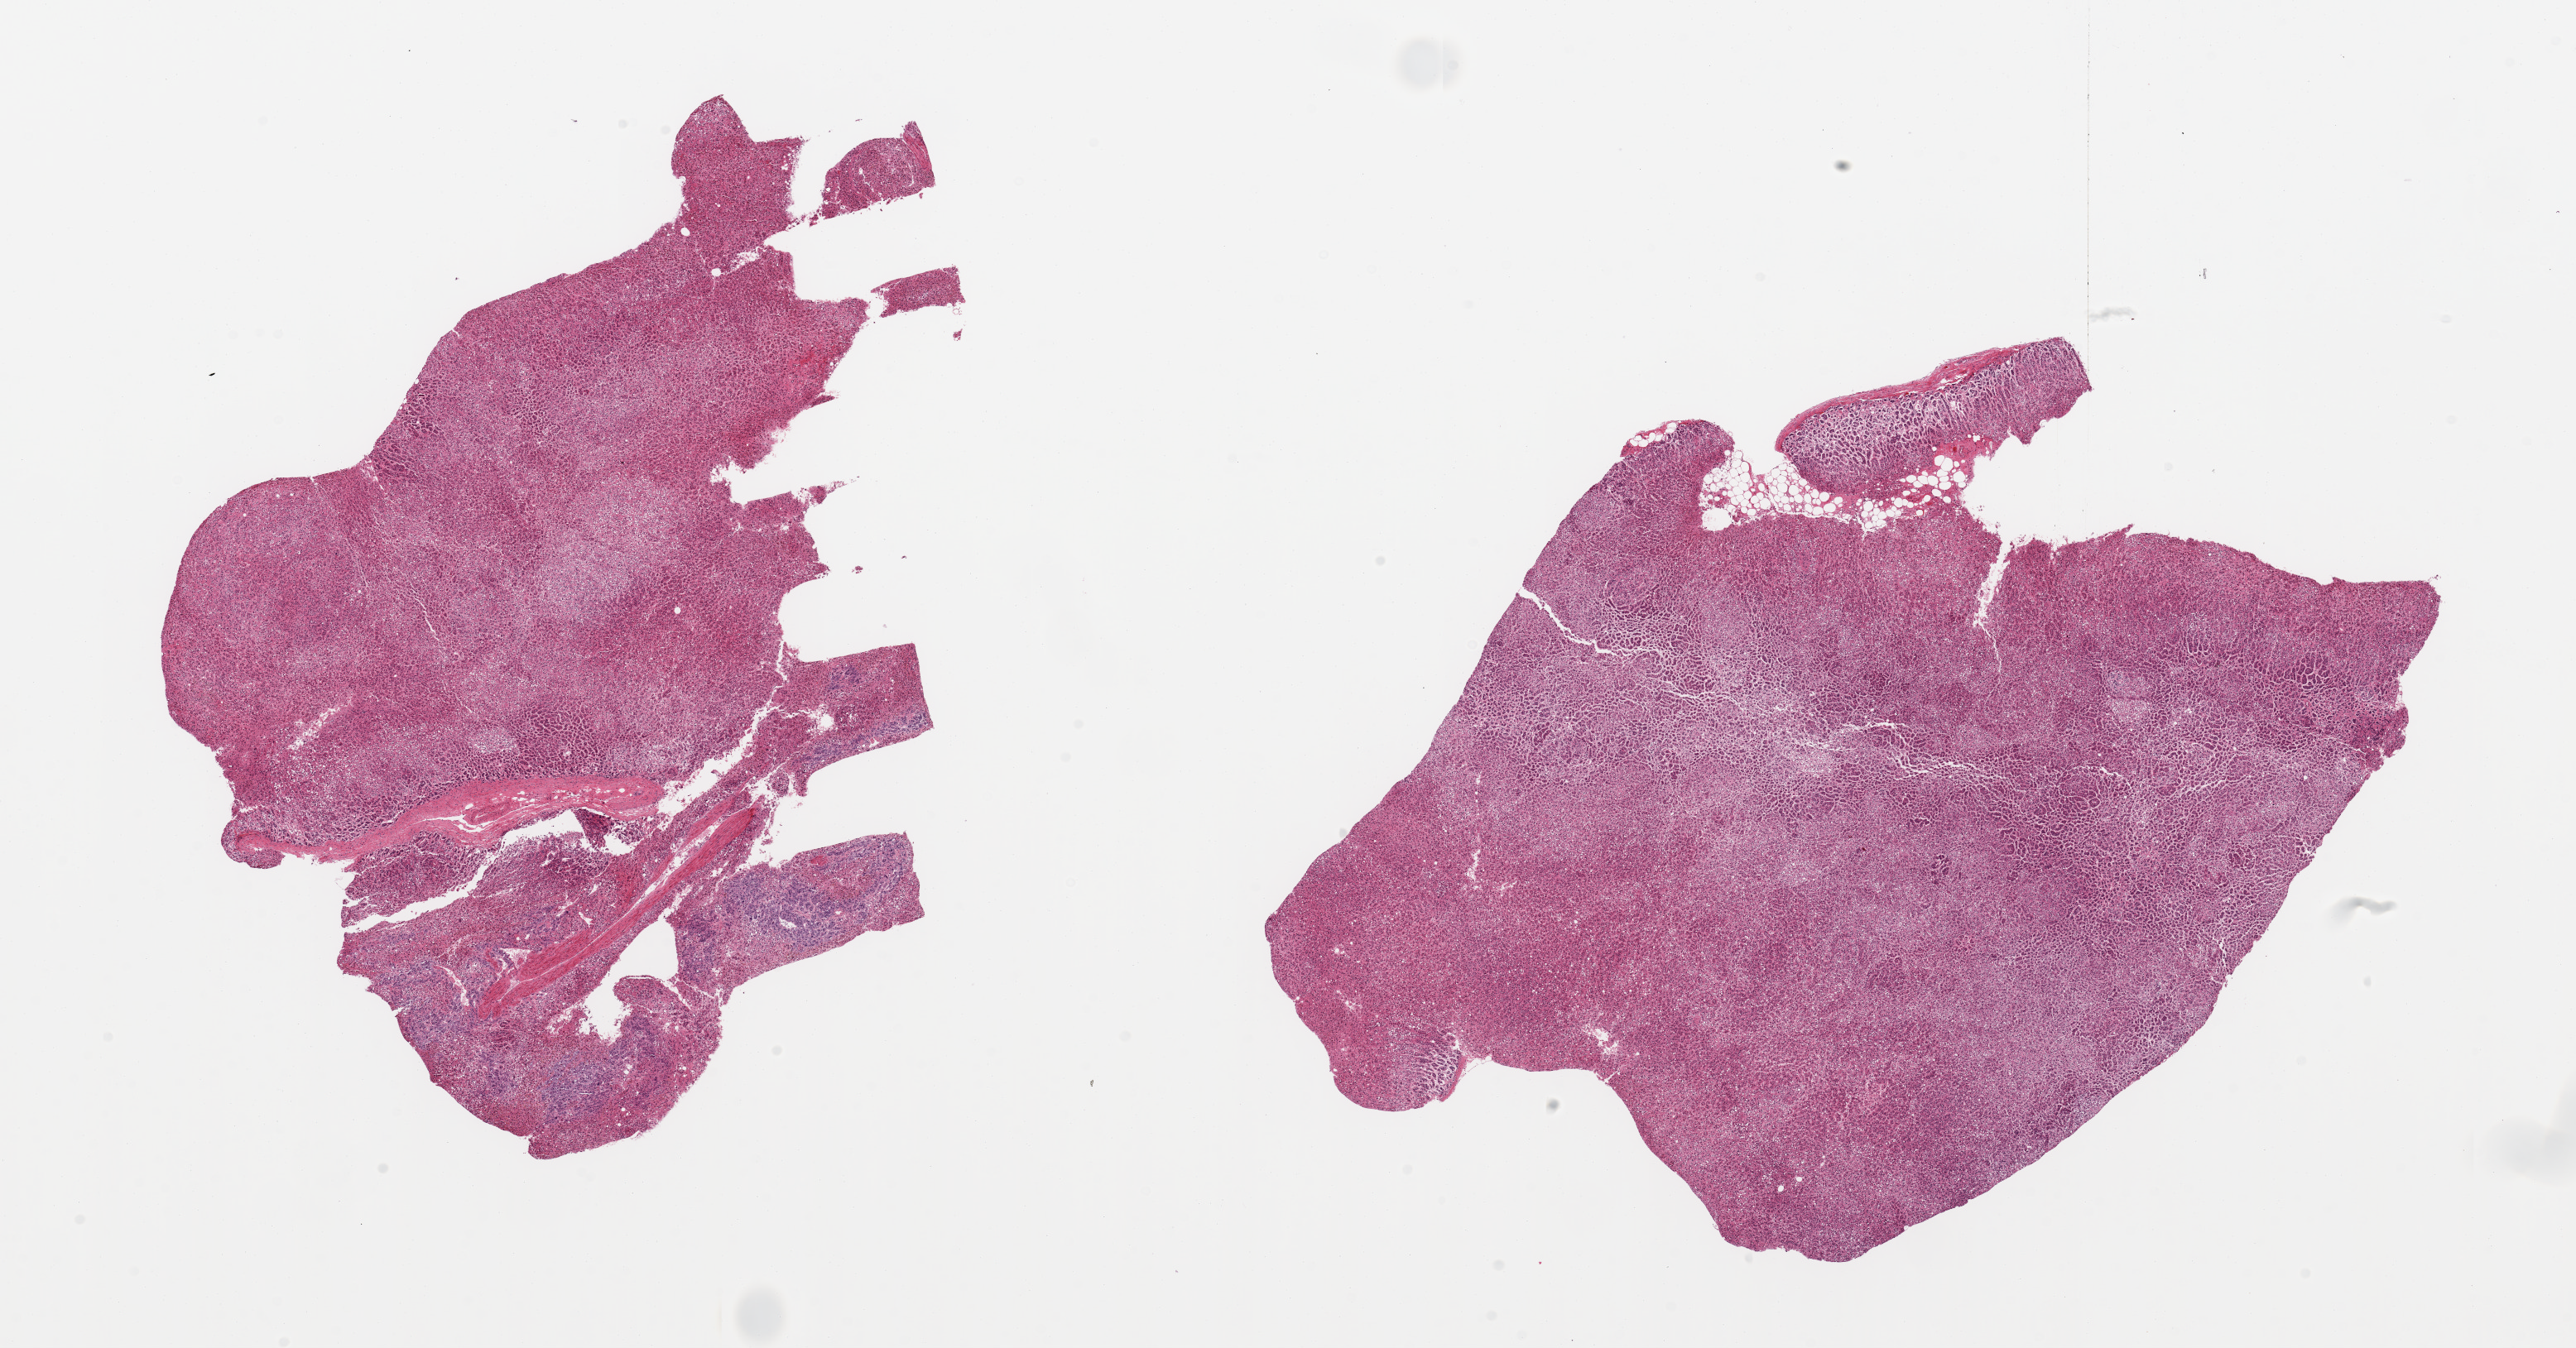
Digitized hematoxylin and eosin (H&E)-stained section, low-resolution overview of the scanned area, about 24.6 x 12.9 mm (from a 20x scan). PAXgene-fixed, paraffin-embedded tissue. Section of adrenal gland (target tissue). Donor tissue sample. Donor sex: male.
Review note (as recorded): 2 pieces; minimal fat content.